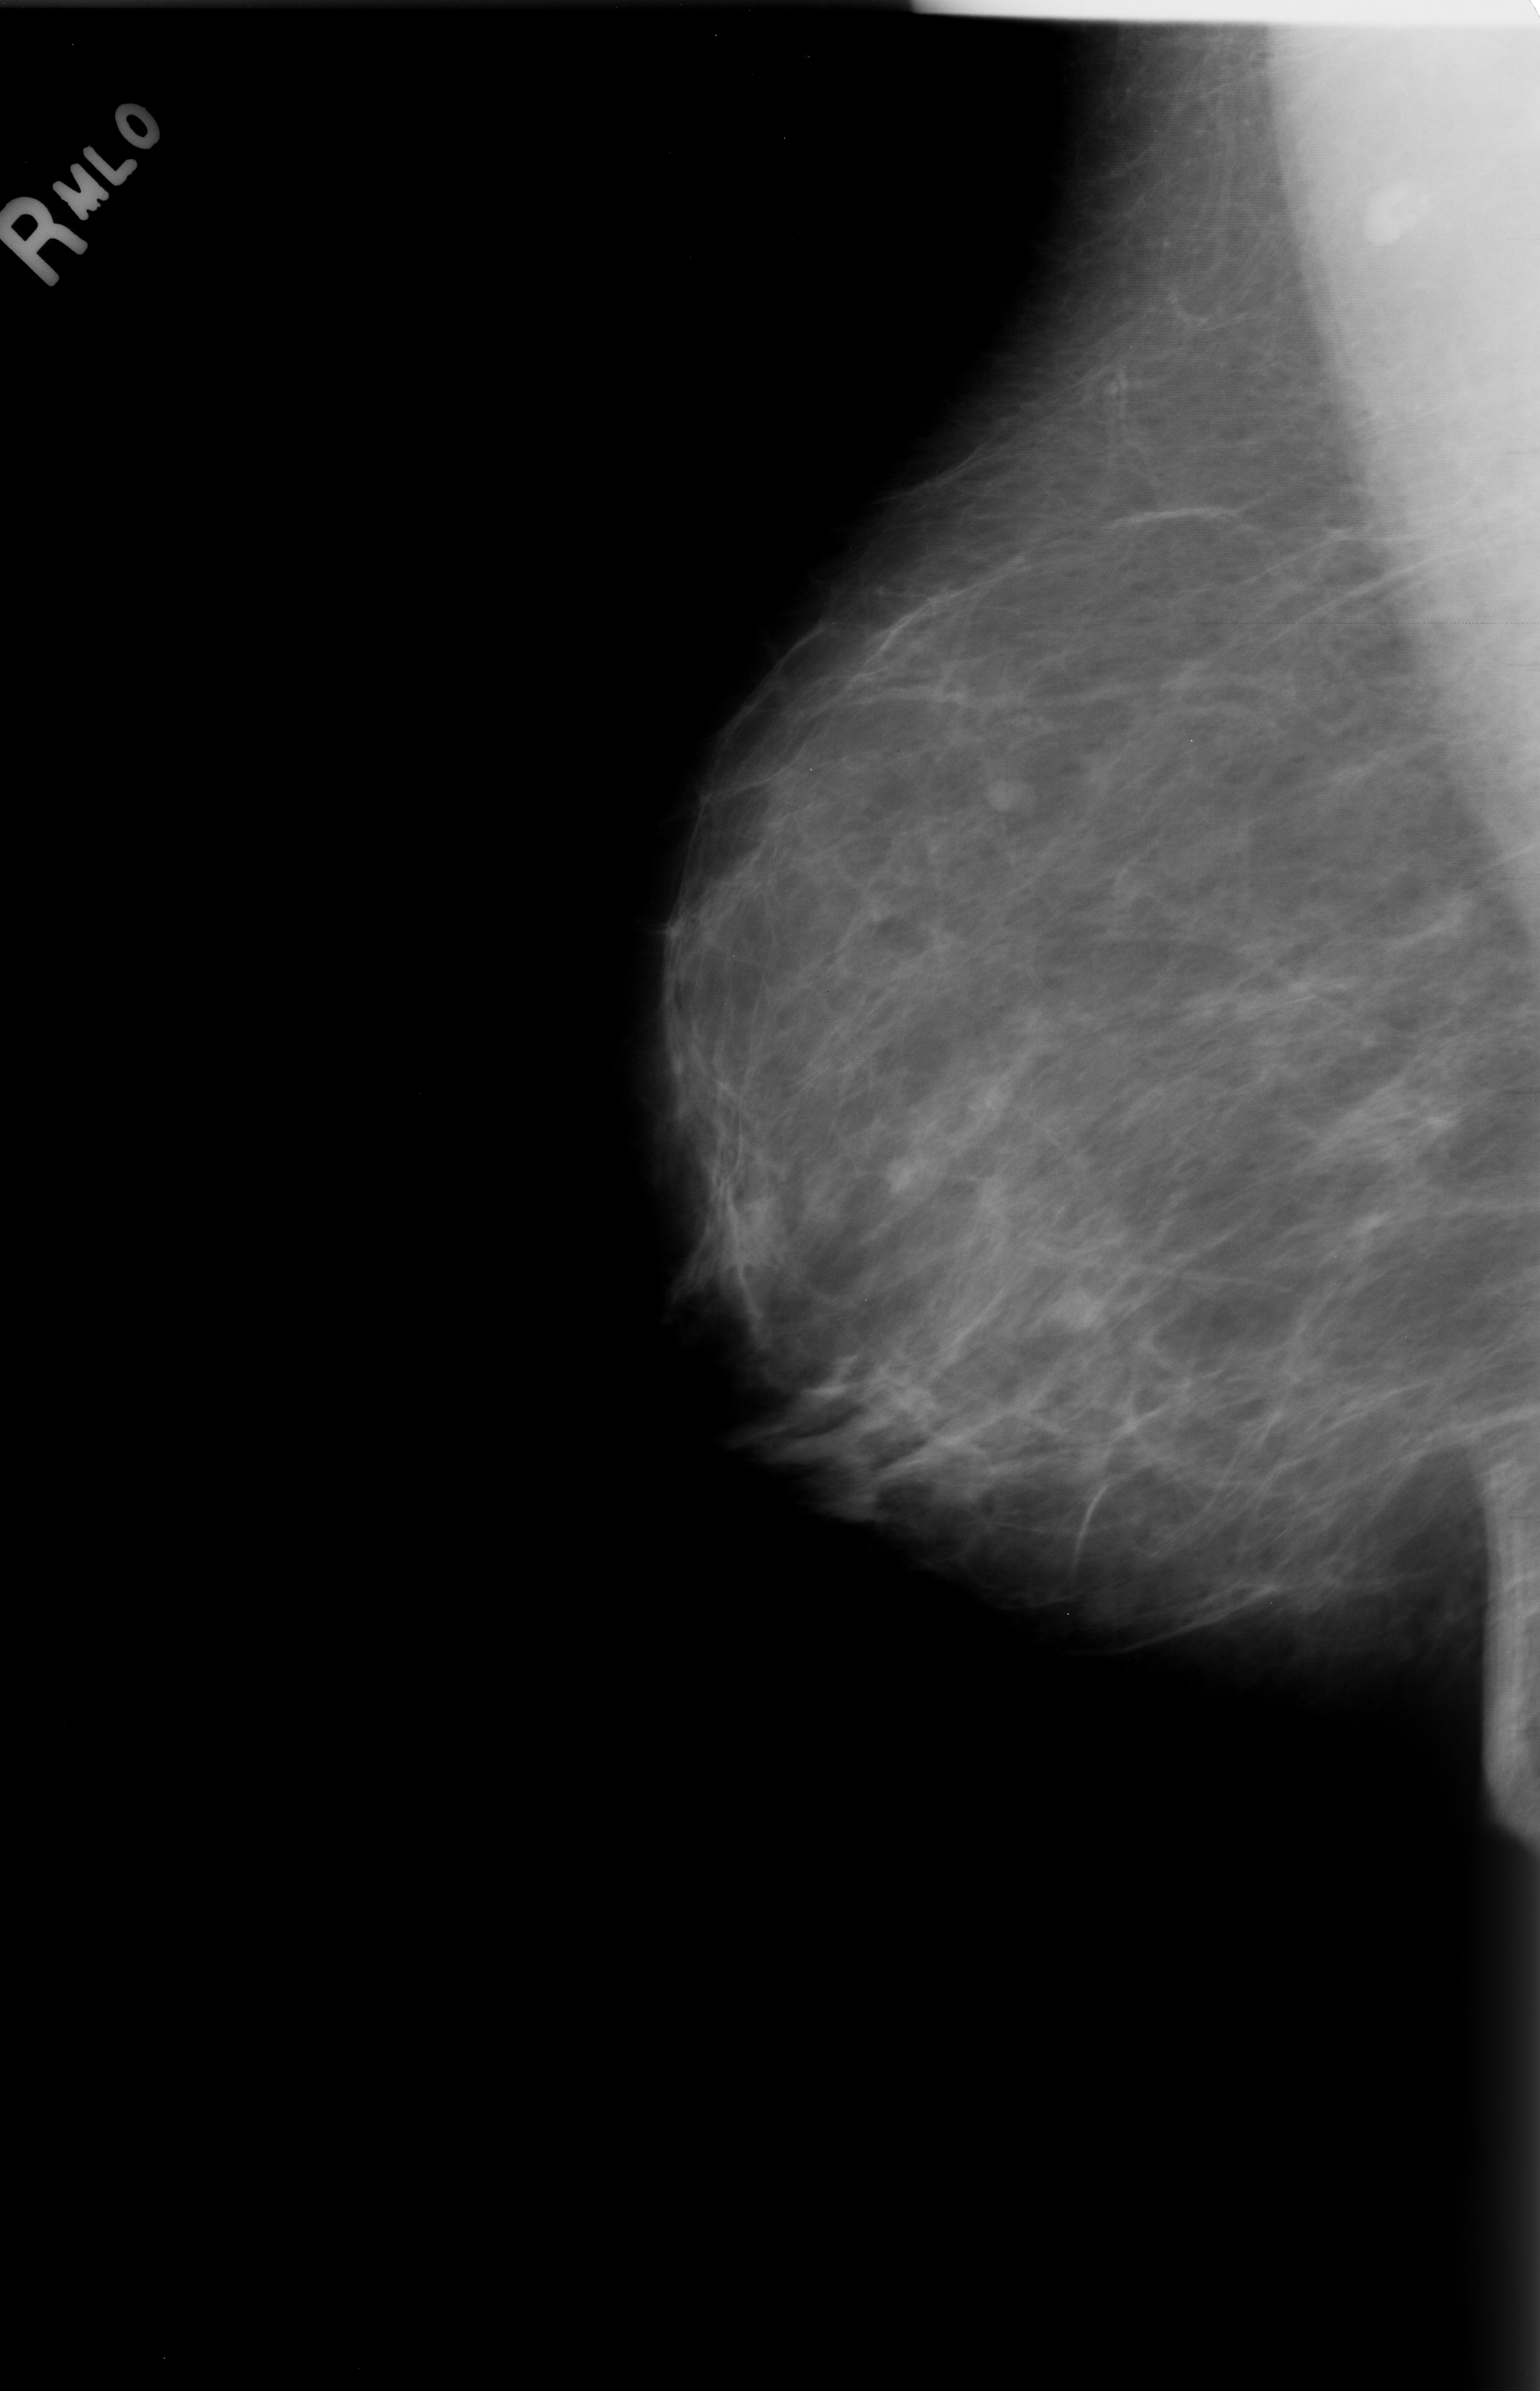
Mammogram (digitized film). Right breast. Mediolateral oblique (MLO) view. Breast composition: almost entirely fatty (BI-RADS density category 1 of 4). 1540 × 2391 image matrix.
Expert-marked regions of interest on this film, with their recorded descriptors:
- mass, shape lobulated, margins obscured; BI-RADS assessment category 3; pathology result (as recorded, not read from the image): benign: box from (x=785, y=1424) to (x=913, y=1525) px